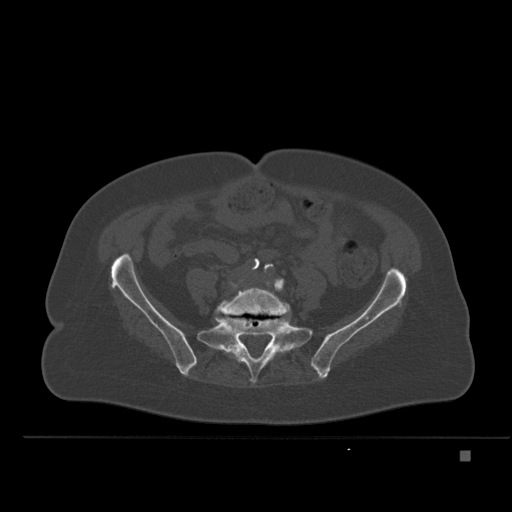
CT including the spine, one axial slice; position 153 of 477 along the scan axis; bone window (W 1800 / L 400 HU); 1.5 mm slice thickness; 512 × 512 image matrix, field of view 422 × 422 mm. Patient: female, 74 years. From the clinical record (not read from this slice): primary cancer: colon.
Structures marked on this image (semi-automatically segmented with operator editing):
- L5 vertebra: bounding box [x1, y1, x2, y2] px = [215, 278, 291, 354]